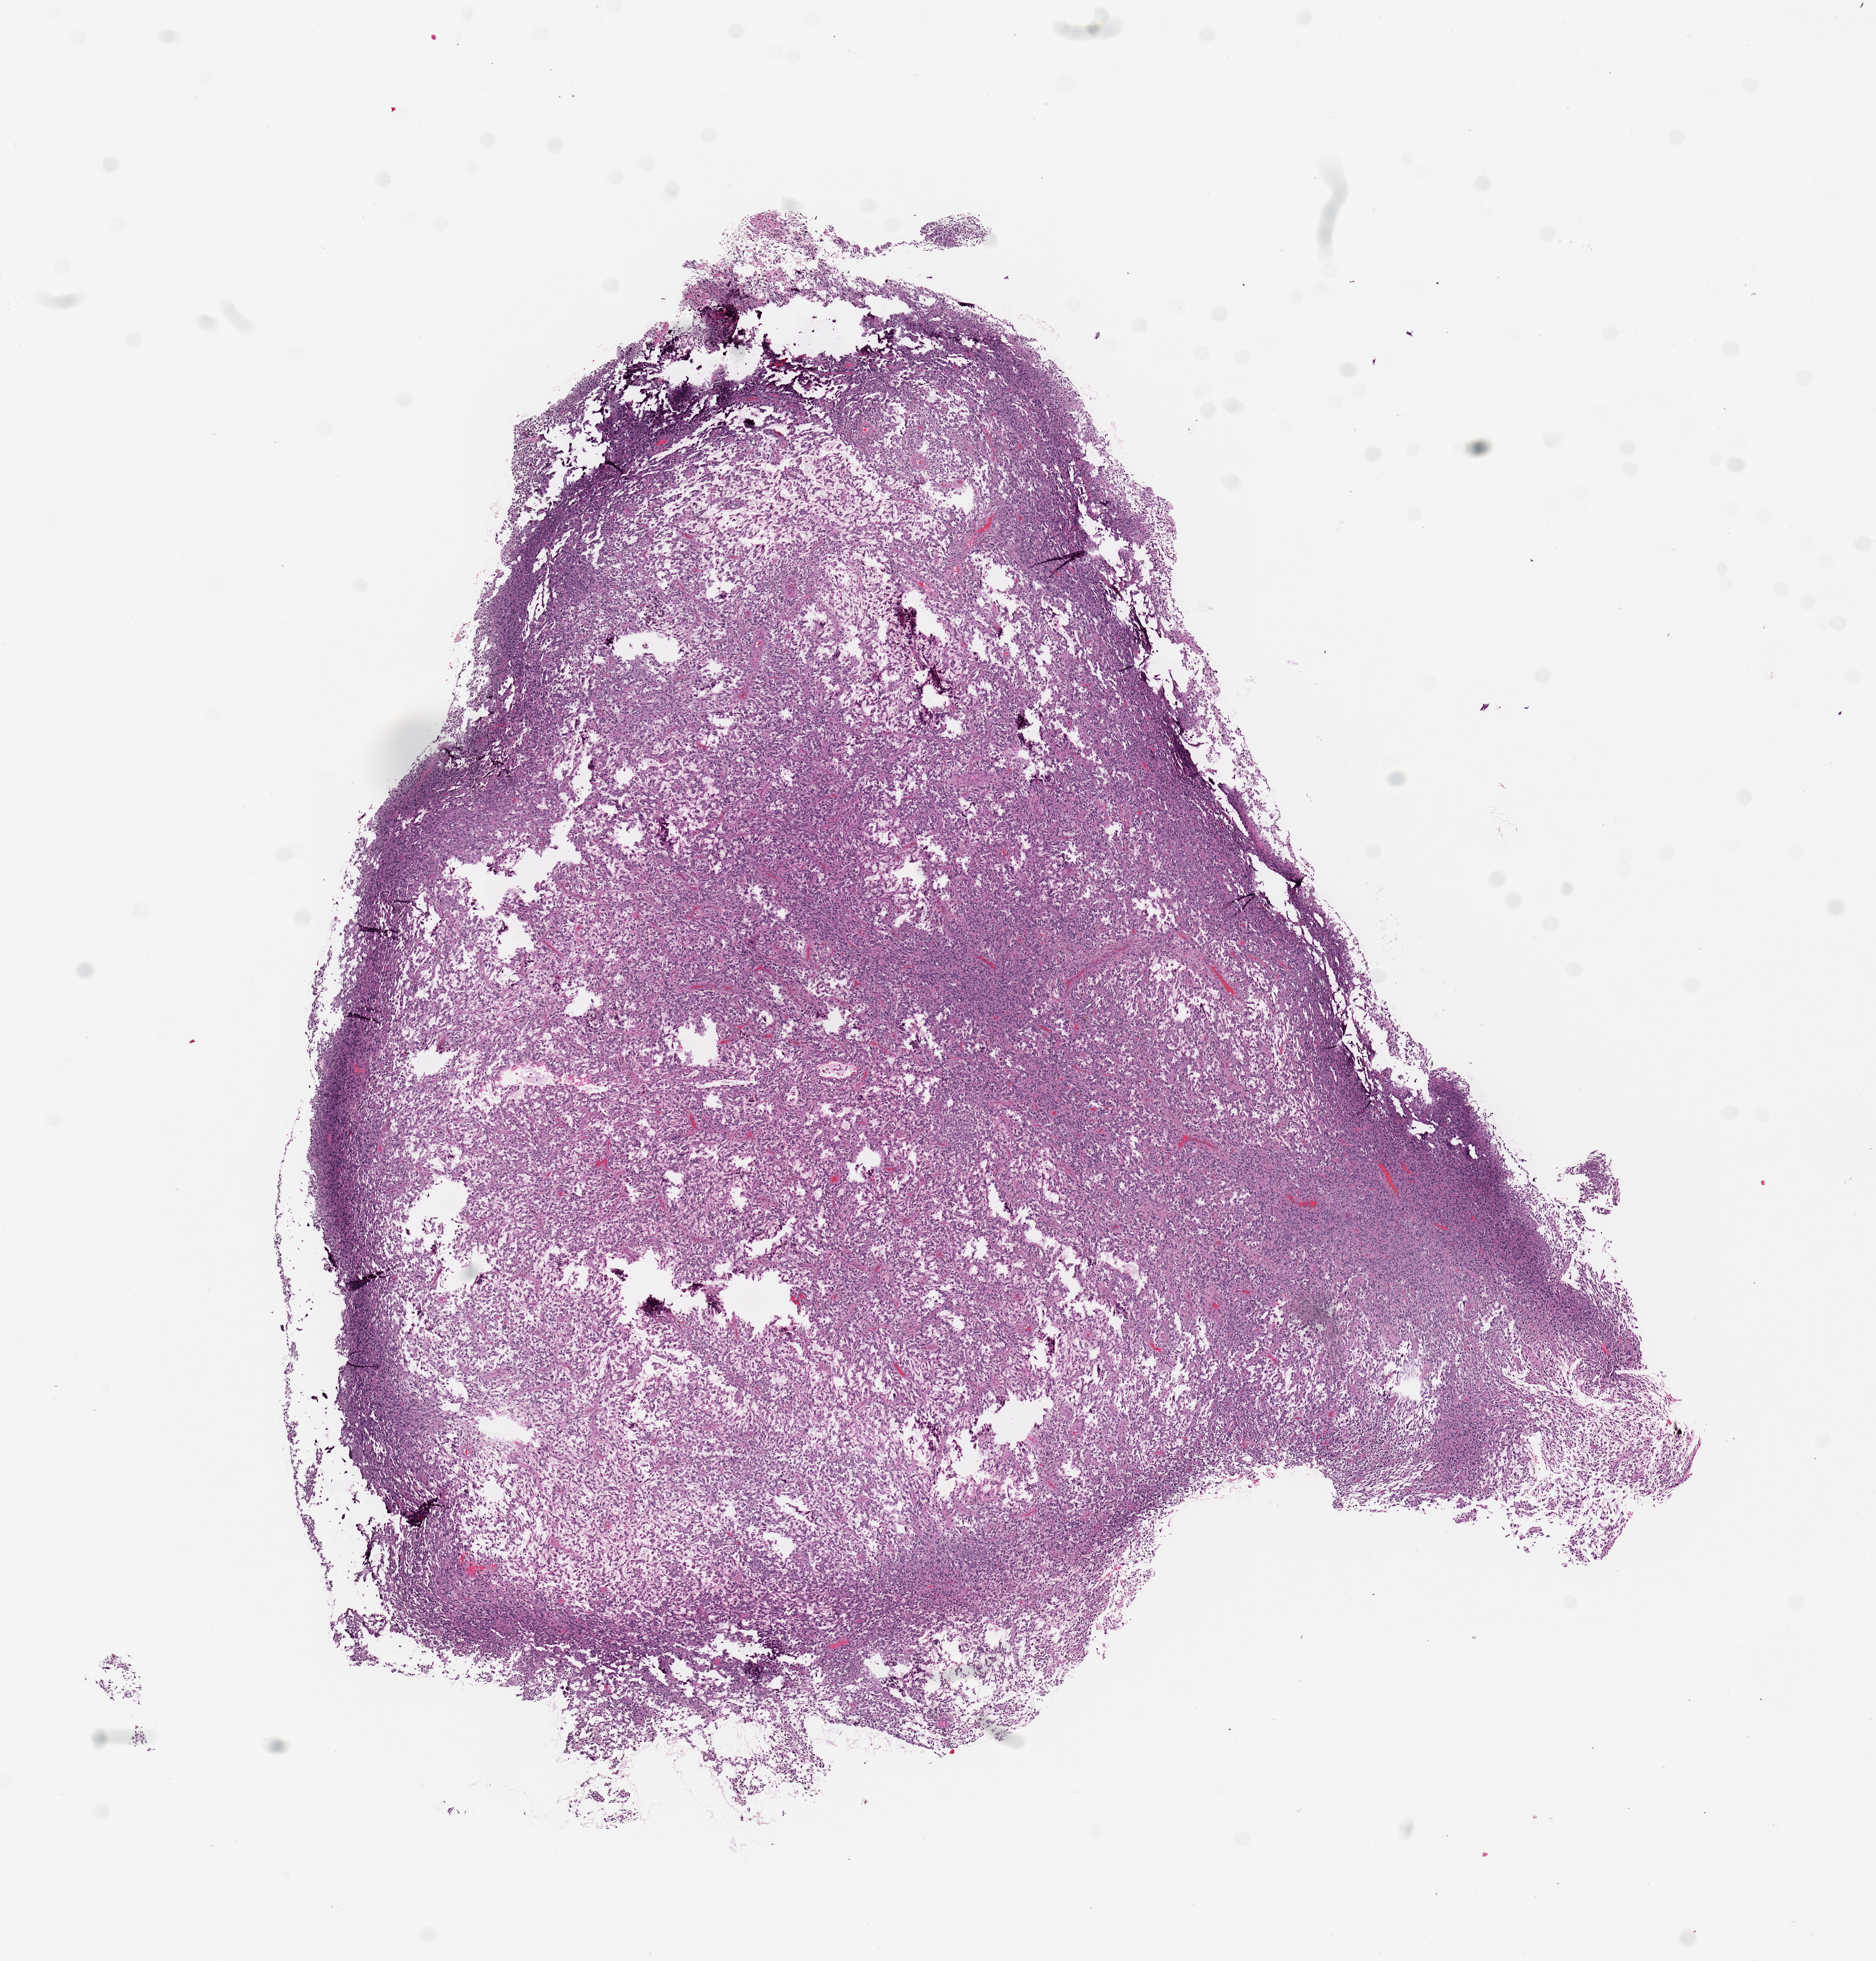
H&E-stained whole-slide image, whole scanned area (about 11.8 x 12.3 mm) shown as a low-resolution overview. Tumour tissue sample. 78-year-old male patient.
Primary tumour site (as recorded): upper extremity. Patient diagnosis (cohort enrolment): sarcoma (site not recorded at cohort level).